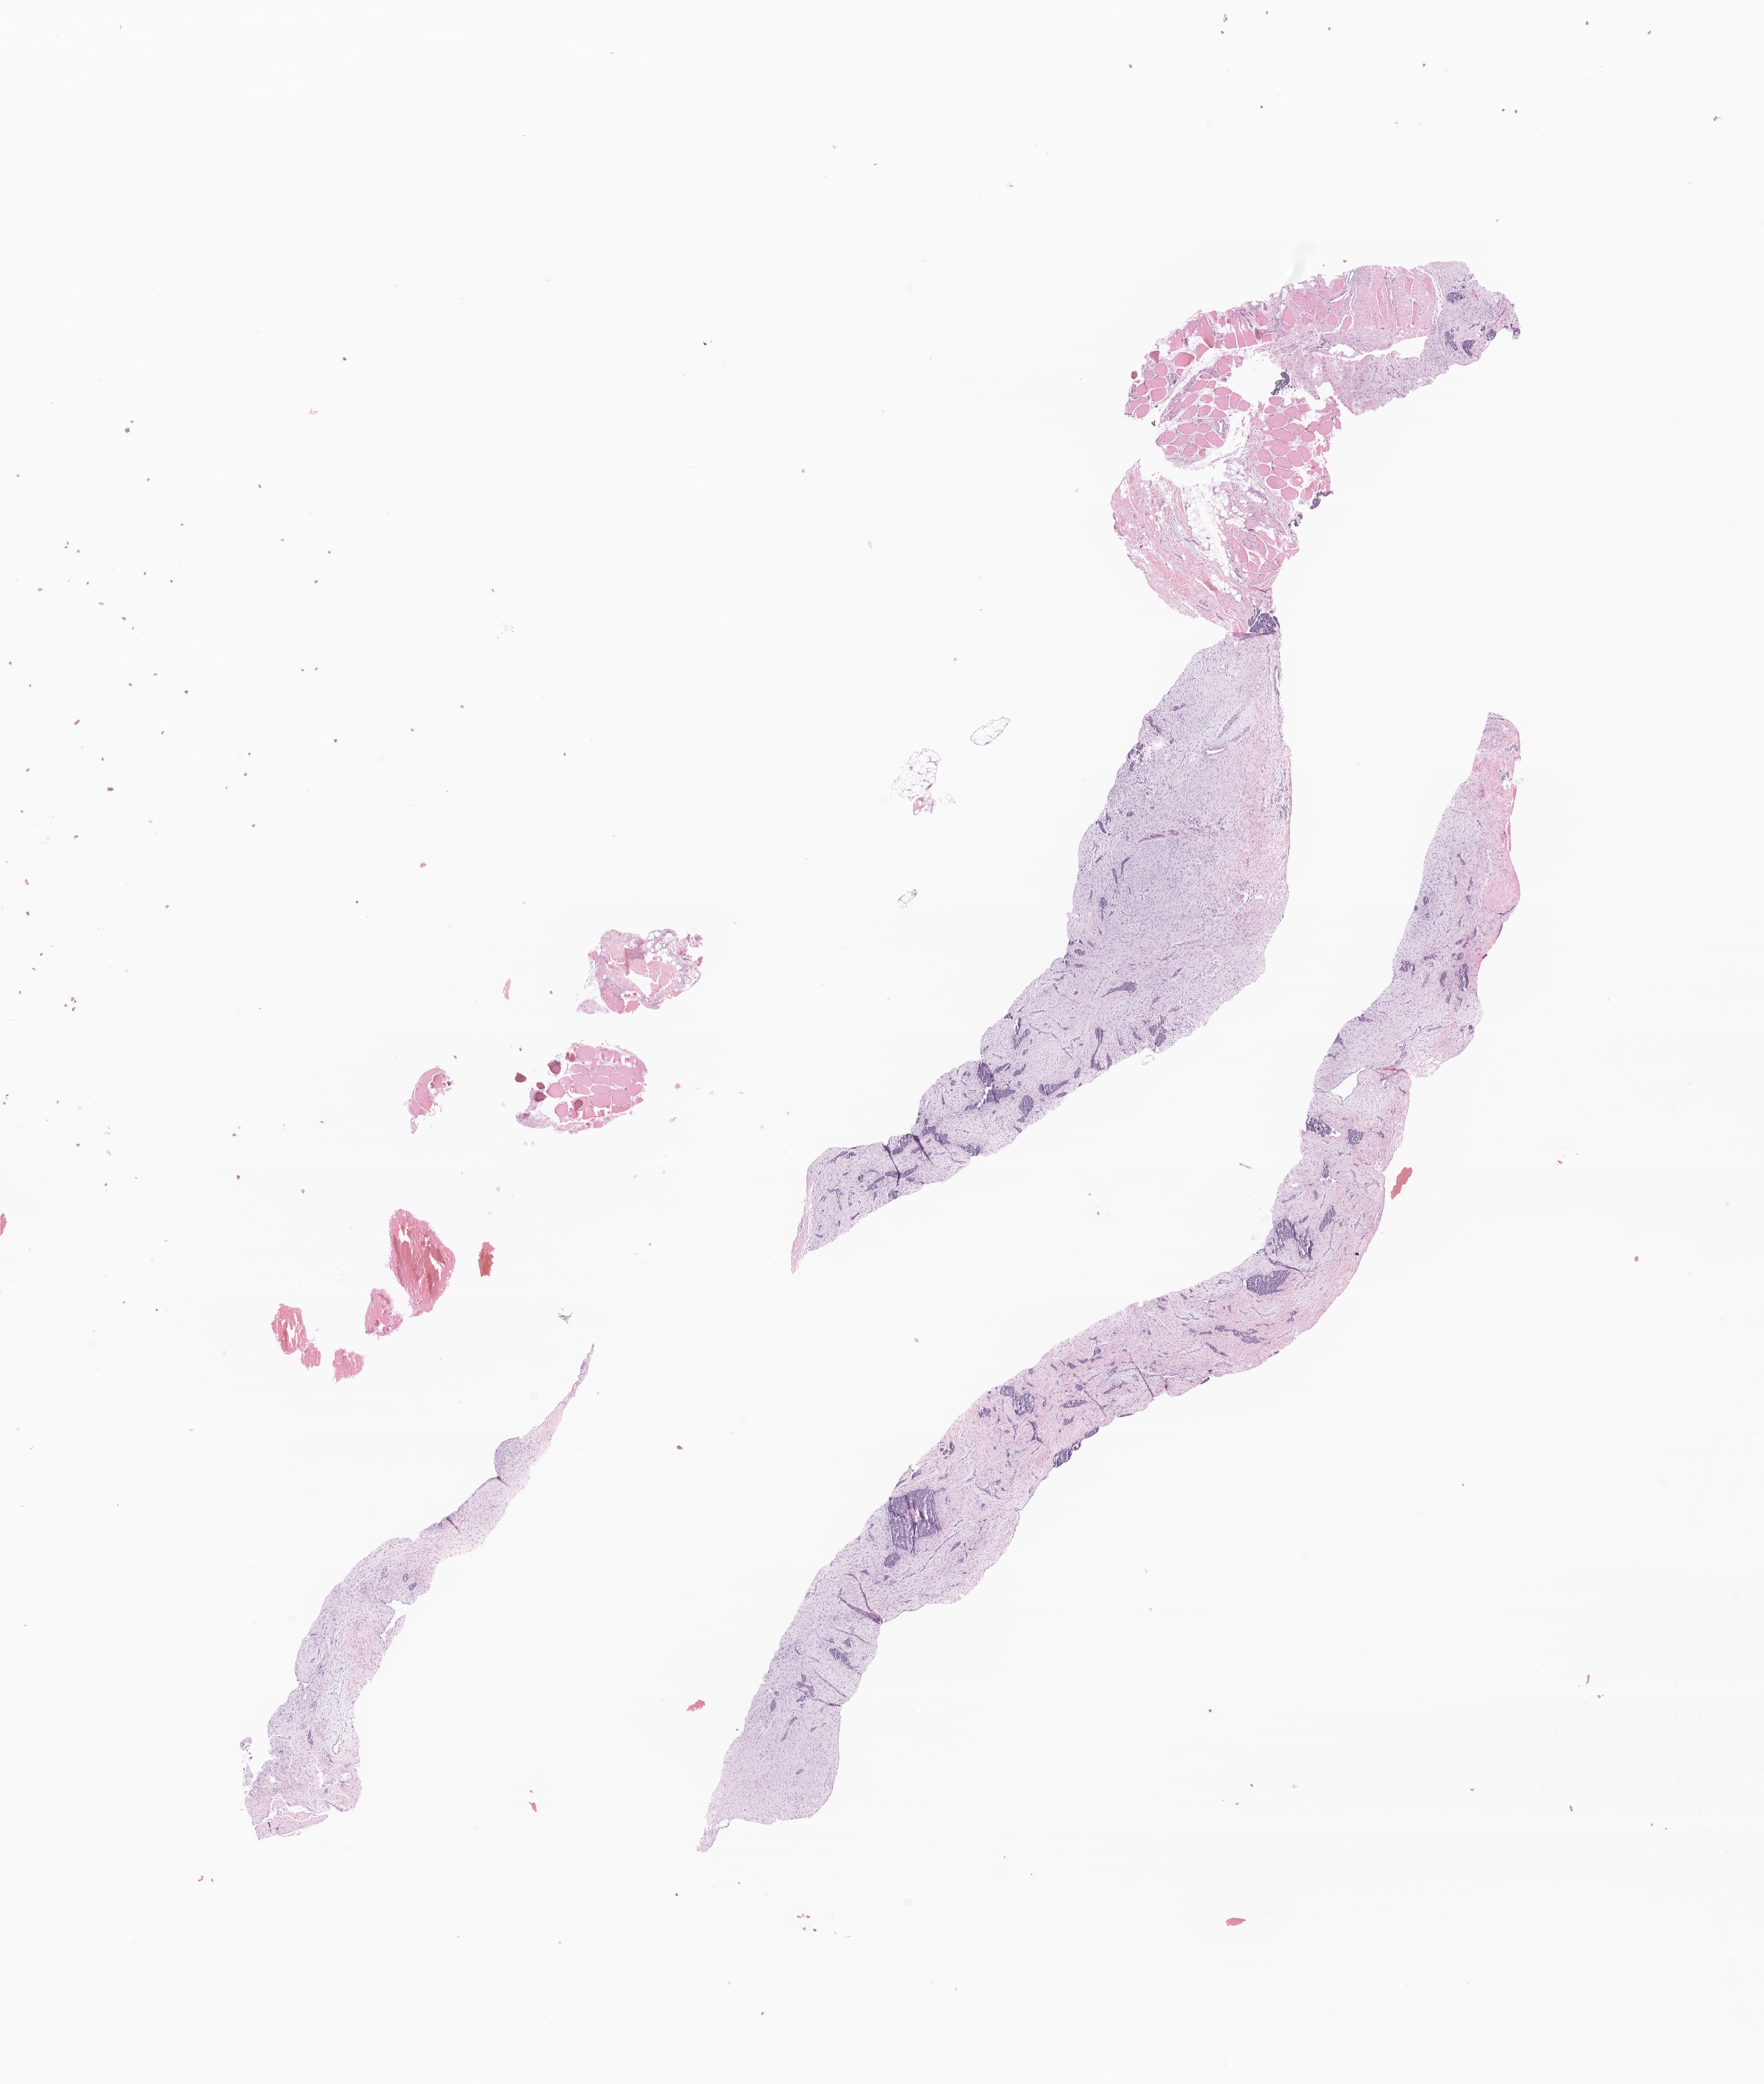
Whole-slide image, H&E stain of tumor tissue from the soft tissue of upper extremity — whole scanned area (about 14.2 x 16.8 mm) shown as a low-resolution overview; FFPE section. Patient: male, age 204 months (17 years).
- recorded diagnosis: Desmoplastic small round cell tumor